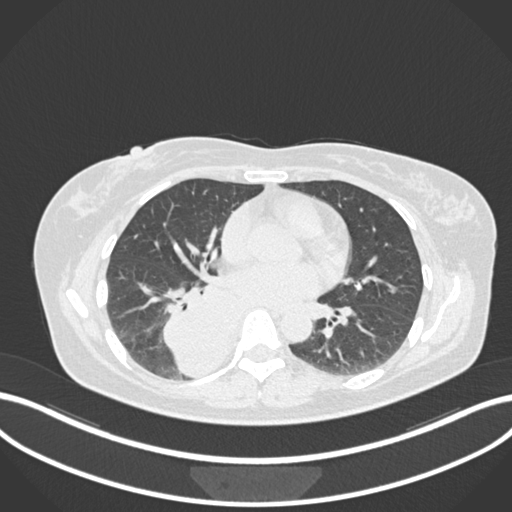
Chest CT, one axial slice. Slice 579 of 677 in the series (ordered by position). Lung window (W 1500 / L -600 HU). 1 mm slice thickness. 512 × 512 image matrix. Female patient, age 54 years. Case-level facts recorded for this patient, not image findings: clinical TNM (as recorded): T4 N0 M0.
Structures marked on this image (bounding box drawn by a radiologist):
- lung tumour (recorded histology: adenocarcinoma): bounding box <156,278,239,377> (left, top, right, bottom; pixels)